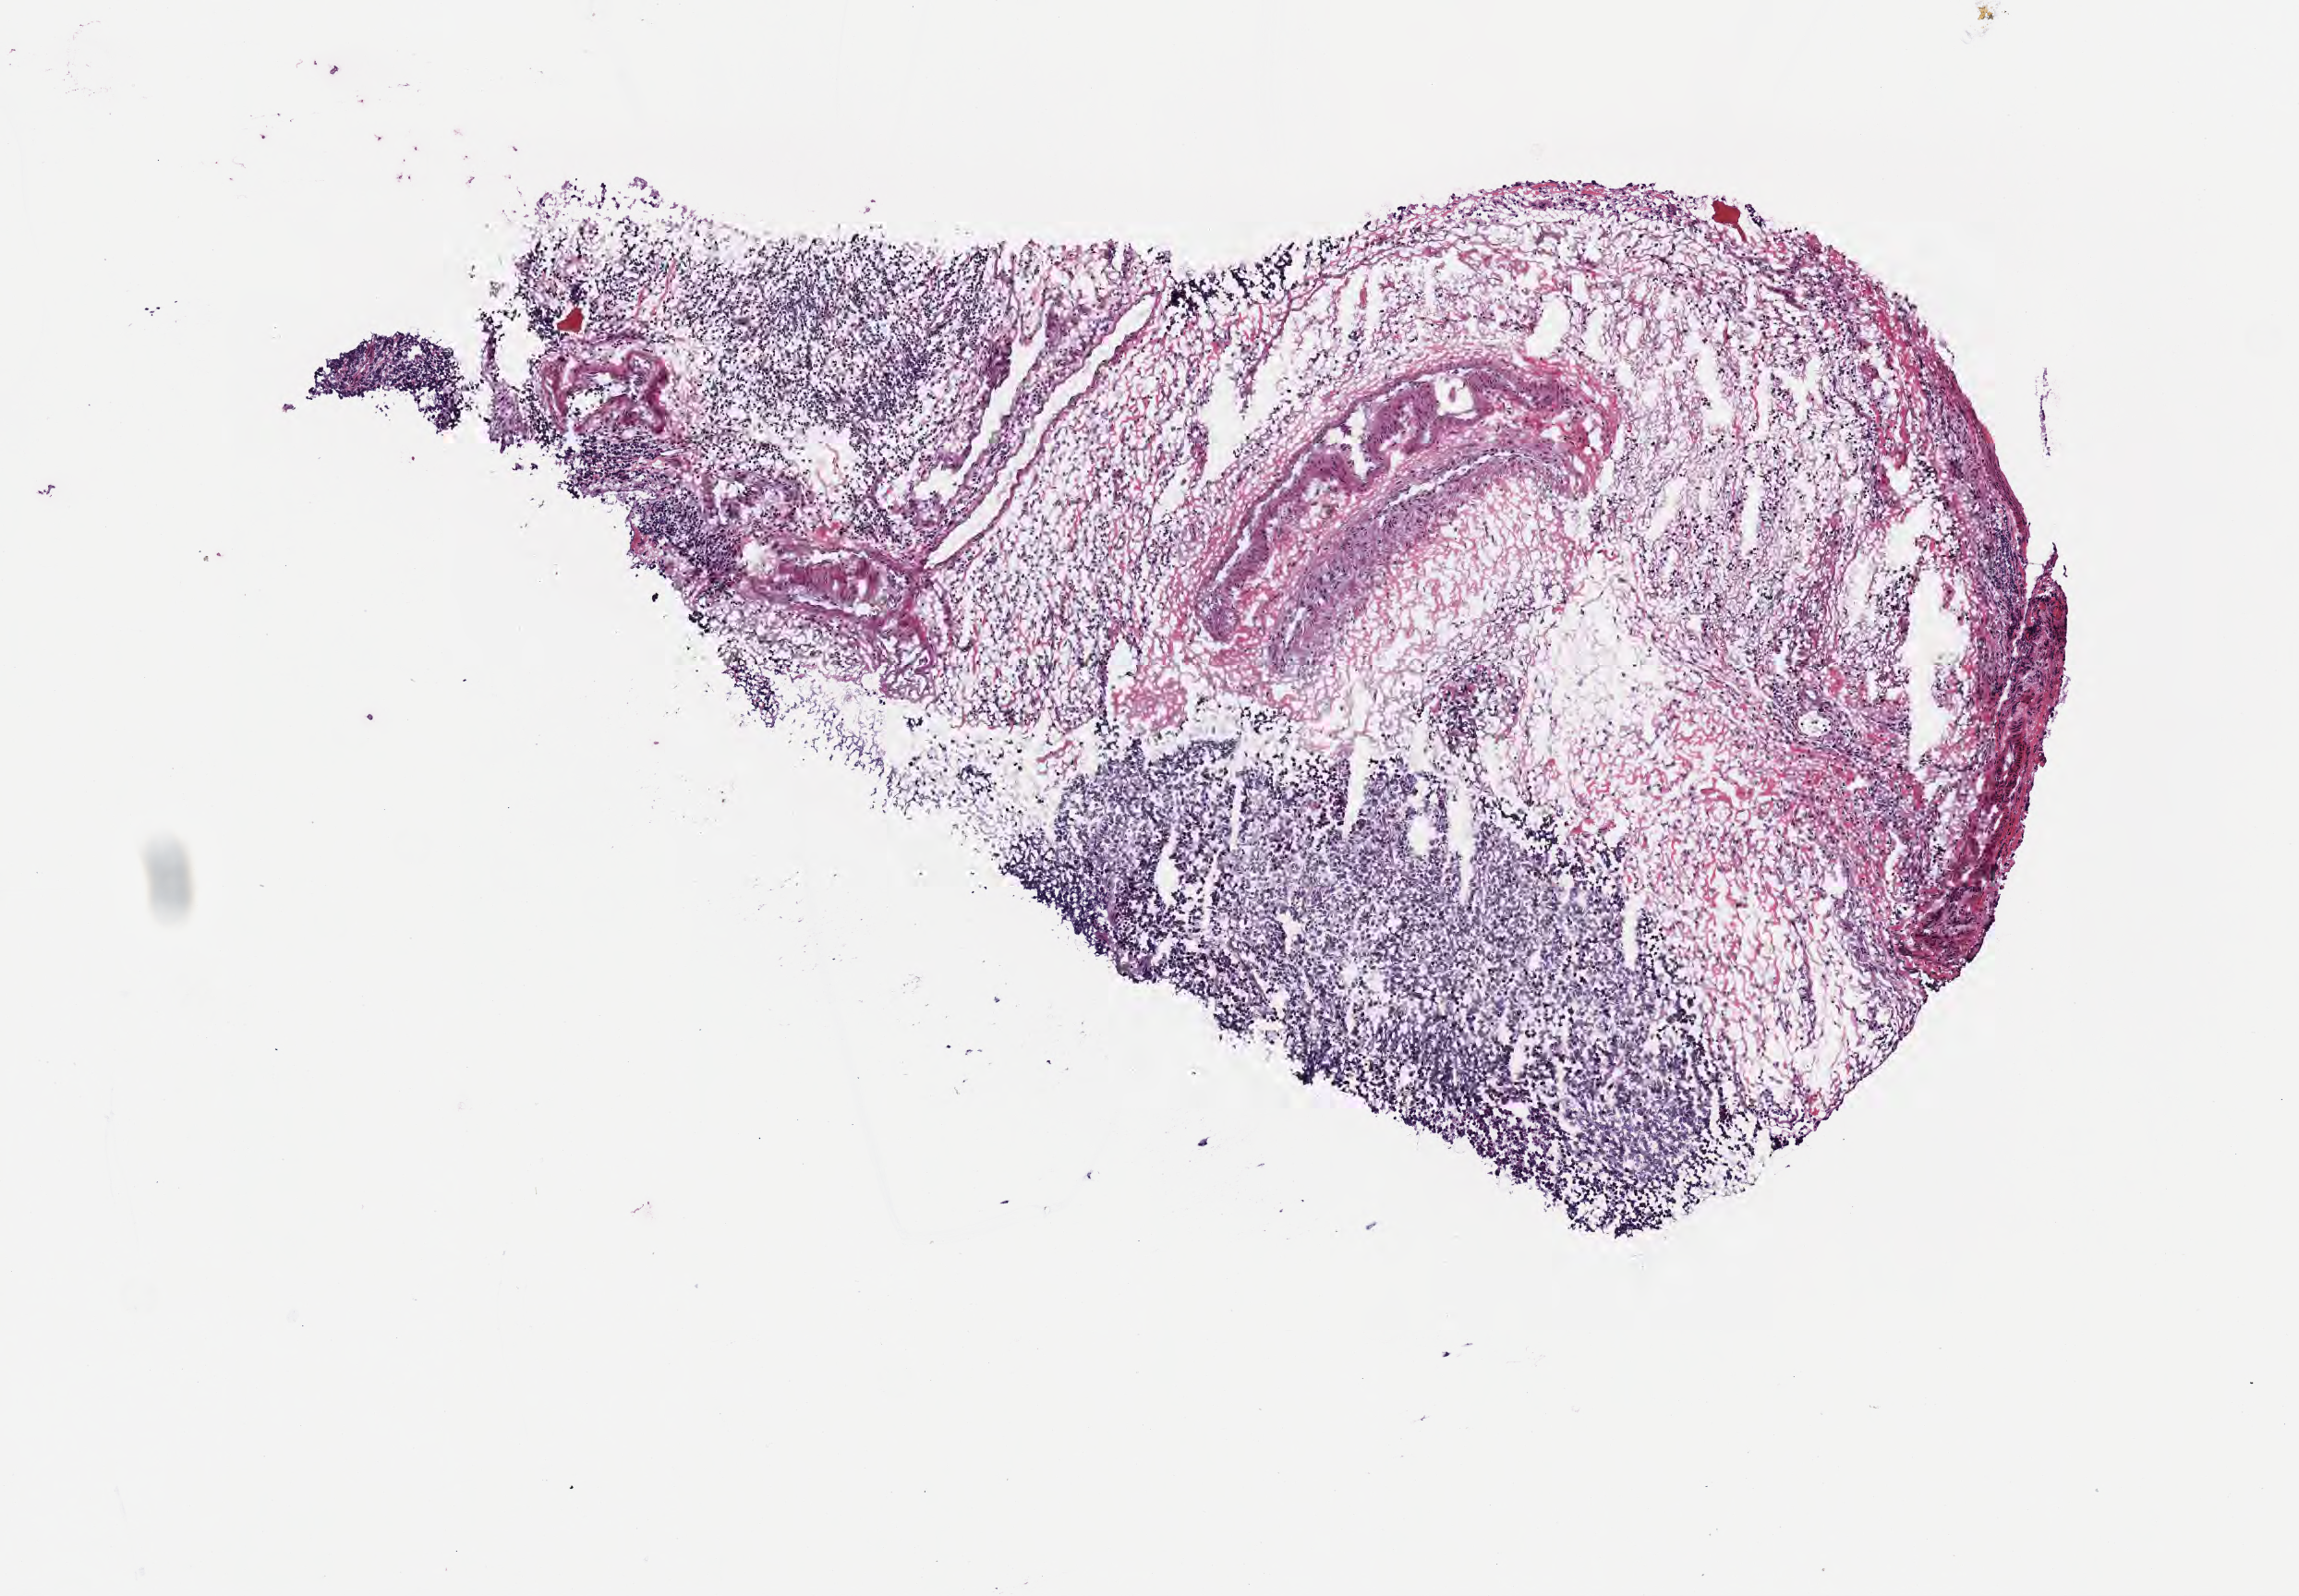
Digitized H&E-stained section, whole scanned area (about 5.0 x 3.5 mm) shown as a low-resolution overview, frozen section (tissue freezing medium), specimen: primary tumor, site: kidney. Female, age 8 years at initial diagnosis. Composition of this section per pathologist review: tumor cells 20%, tumor nuclei 50%, stromal cells 25%, necrosis 5%, normal cells 50%. Infiltration values recorded for this section: lymphocyte infiltration 70%, monocyte infiltration 10%, neutrophil infiltration 10%.
Diagnosis: Burkitt lymphoma, NOS. Ann Arbor stage (patient): Stage IV. Section: top of the tissue portion.